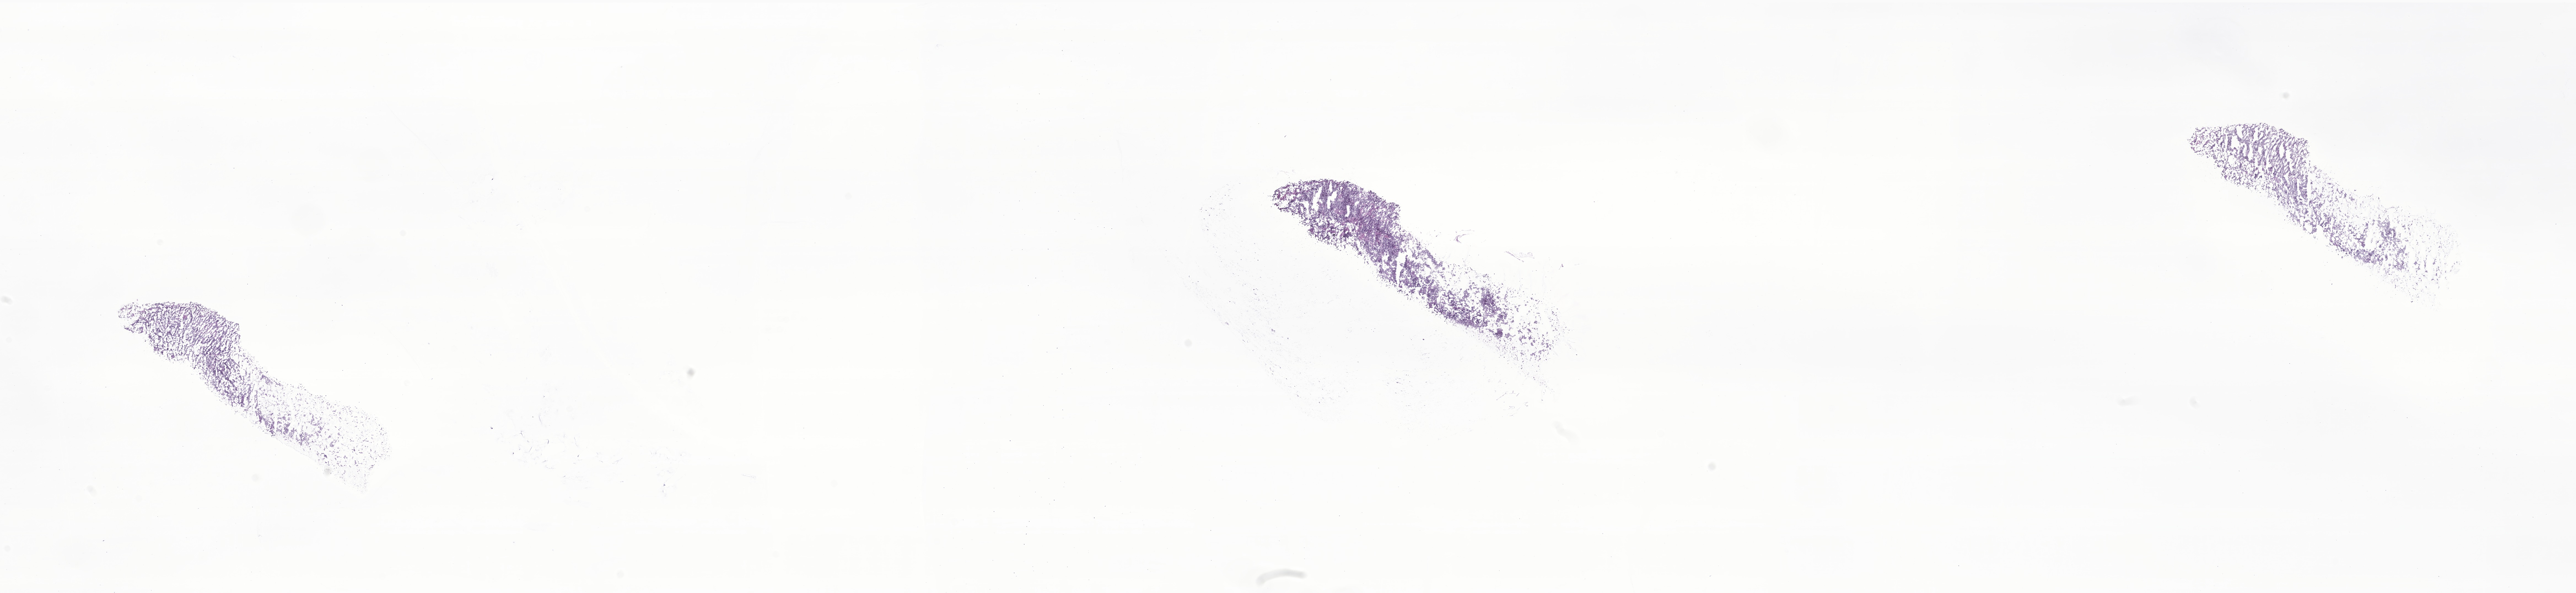
Whole-slide image, hematoxylin and eosin (H&E) stain of tumor tissue from the soft tissue of abdomen — whole scanned area (about 39.4 x 9.1 mm) shown as a low-resolution overview. Cryosection (OCT / tissue freezing medium). Female patient, age 685 days (about 1.9 years).
Diagnosis: Neuroblastoma, NOS. Tissue or organ of origin (case record): connective, subcutaneous and other soft tissues of abdomen.